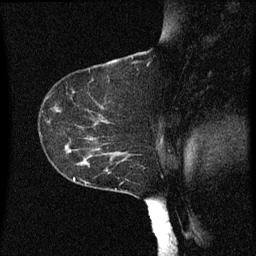
Breast MRI (dynamic contrast-enhanced), one sagittal slice; slice 41 of 60 in the series (ordered by position); dynamic contrast-enhanced series, image 2 of 3 at this slice position (ordered by acquisition); 1.5 T; TE 4.2 ms, TR 8 ms; 2 mm slice thickness; 256 × 256 image matrix, field of view 200 × 200 mm. Female patient, age 55 years.
Structures marked on this image (semi-automatic segmentation, software-assisted and operator-edited):
- analysis volume of interest (the breast-tissue region the enhancement analysis was run in; not a lesion): bounding box <46,124,151,173> (left, top, right, bottom; pixels)
- tumour enhancement mask (voxels above the 70 % enhancement threshold inside the analysis volume of interest): <70,138,125,157>